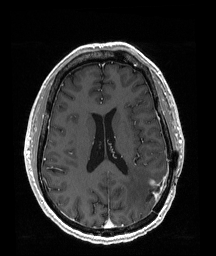
Brain MRI from a brain-tumour surgery series, one axial slice; T1-weighted post-contrast; 216 × 256 image matrix. From the clinical record (not read from this slice): histopathology: Glioblastoma; WHO grade: 4; IDH mutation: no; tumour location: Left Temporoparietal.
Annotated regions visible in this slice (outlined manually by an expert reader):
- tumour: box from (x=151, y=181) to (x=158, y=196) px